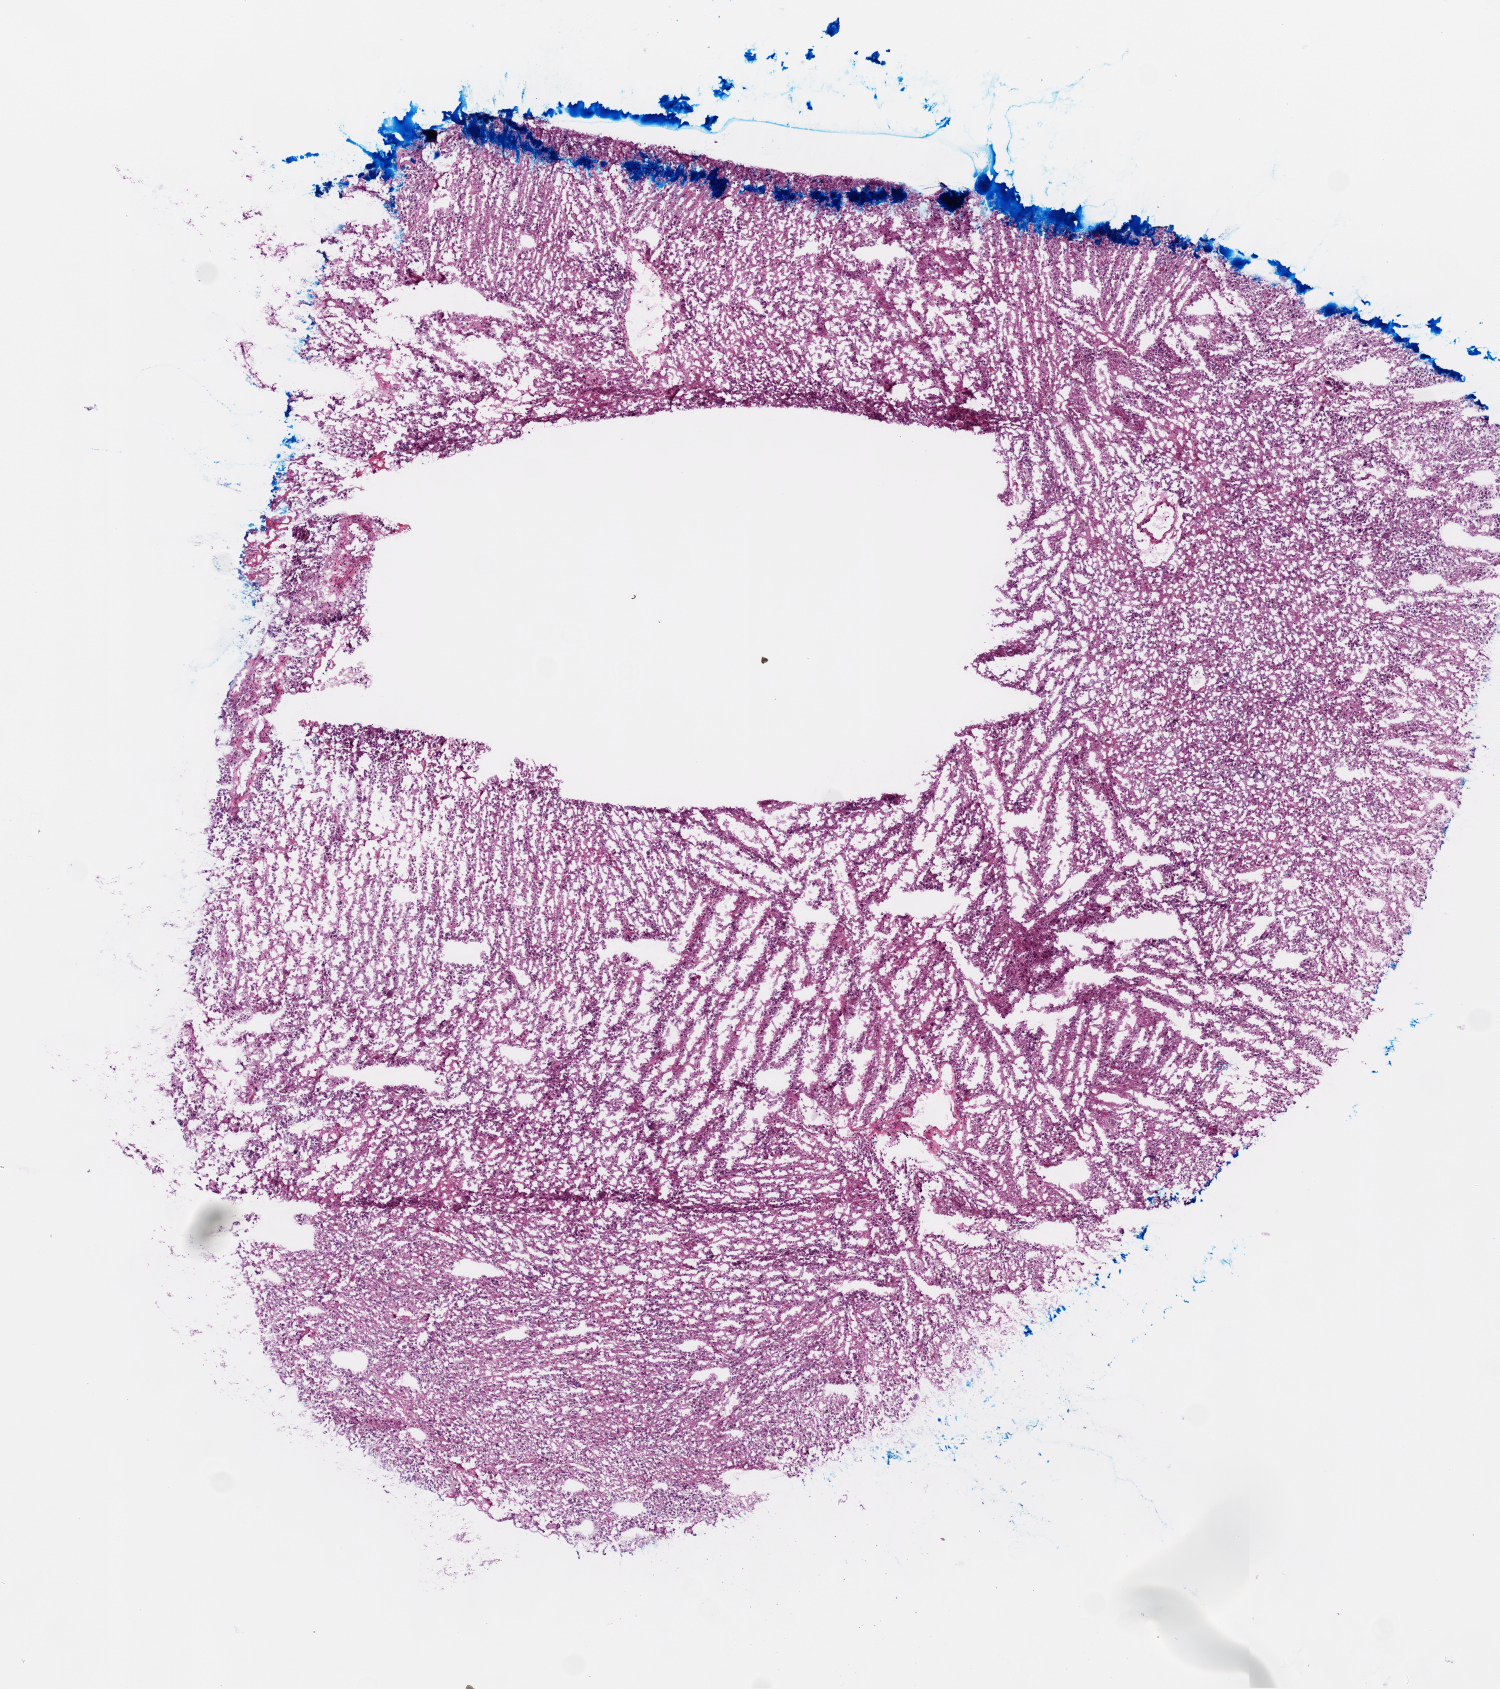
H&E-stained whole-slide image — low-resolution overview of the scanned area, about 6.0 x 6.8 mm, frozen section, brain, primary tumour sample. Male, age 48 years at initial diagnosis. Pathologist review of this section (percent, as recorded): tumour cells 100%, tumour nuclei 85%.
Pathologic diagnosis: Glioblastoma.